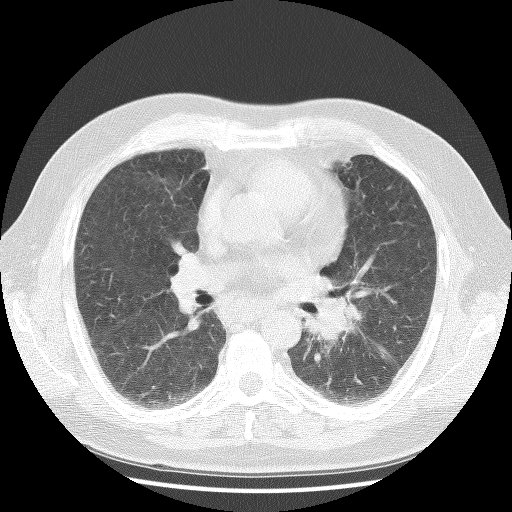
Axial slice from a low-dose chest CT screening exam; first (baseline) screen; lung window (W 1500 / L -600 HU); lung (sharp) reconstruction kernel (BONE); slice 47 of 111 in the series; 512 × 512 image matrix, field of view 350 × 350 mm. Male, age 59 years at enrolment.
Expert-annotated lung lesion, bounding box [x1, y1, x2, y2] px = [300, 286, 378, 363]. Screening reader's record for this exam (one nodule recorded; not confirmed to be the boxed lesion): non-calcified nodule or mass ≥4 mm, right upper lobe, 4 × 4 mm, soft tissue attenuation. Note: the box lies in the patient's left hemithorax on this image, whereas the reader's record names the right lung; they may be different findings. Lung cancer was diagnosed 20 days after this screen: non-small cell carcinoma, left hilum, stage IV (AJCC 6th edition).